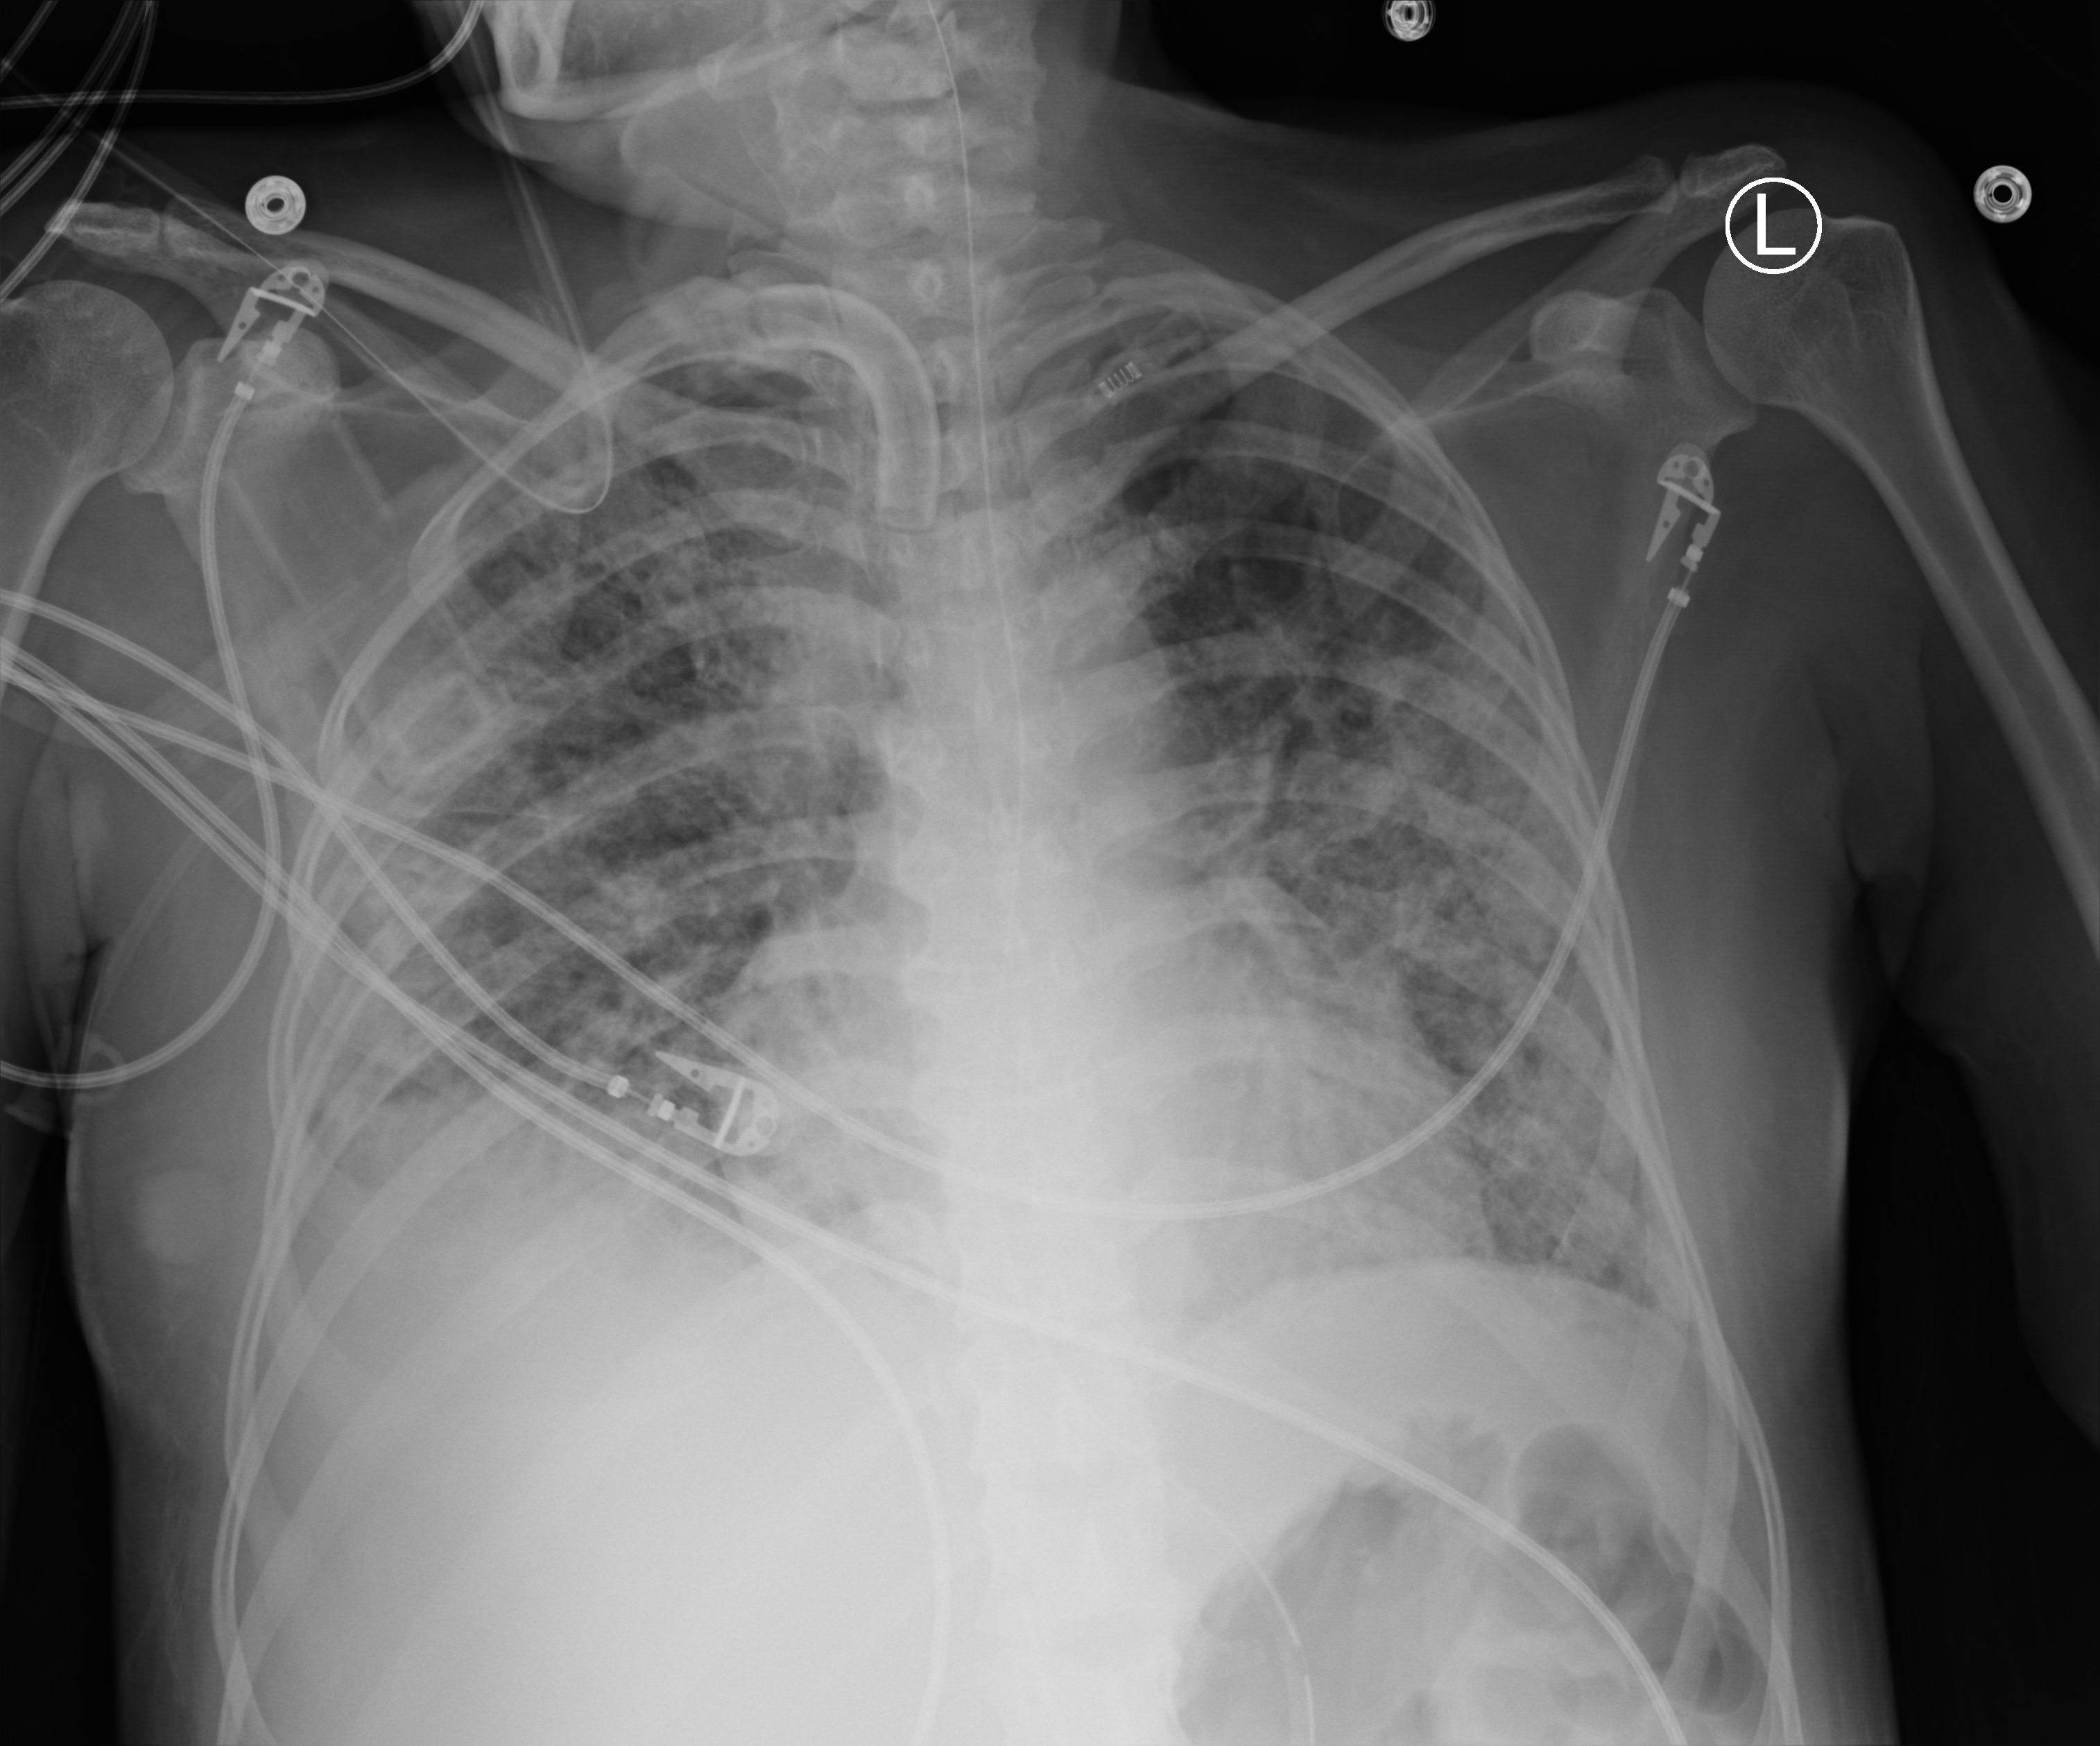
Portable chest radiograph; anteroposterior (AP) projection. Female patient hospitalised with COVID-19, age 18–59 years.
Hospital-stay facts (about this admission, not read from this image; timing relative to this image not recorded): mechanically ventilated during this hospital stay: yes.